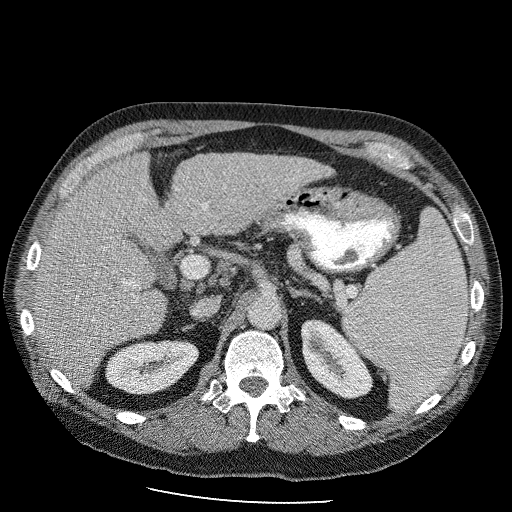
Contrast-enhanced abdominal CT (liver protocol), one axial slice; position 55 of 98 along the scan axis; reconstruction kernel STANDARD; 120 kVp; soft-tissue window (W 400 / L 40 HU); 2.5 mm slice thickness; 512 × 512 image matrix. Case-level facts recorded for this patient, not image findings: diagnosis: hepatocellular carcinoma (patient treated with transarterial chemoembolisation; whether this scan precedes or follows treatment is not stated here); TNM stage (as recorded): Stage-II; Child-Pugh class: B; tumour nodularity: uninodular.
Annotated regions visible in this slice (semi-automatically segmented with operator editing):
- liver parenchyma outside the tumour (the mass and vessels are separate outlines, so this box may not span the whole liver): bounding box <30,151,336,388> (left, top, right, bottom; pixels)
- liver vessels: <129,205,206,288>